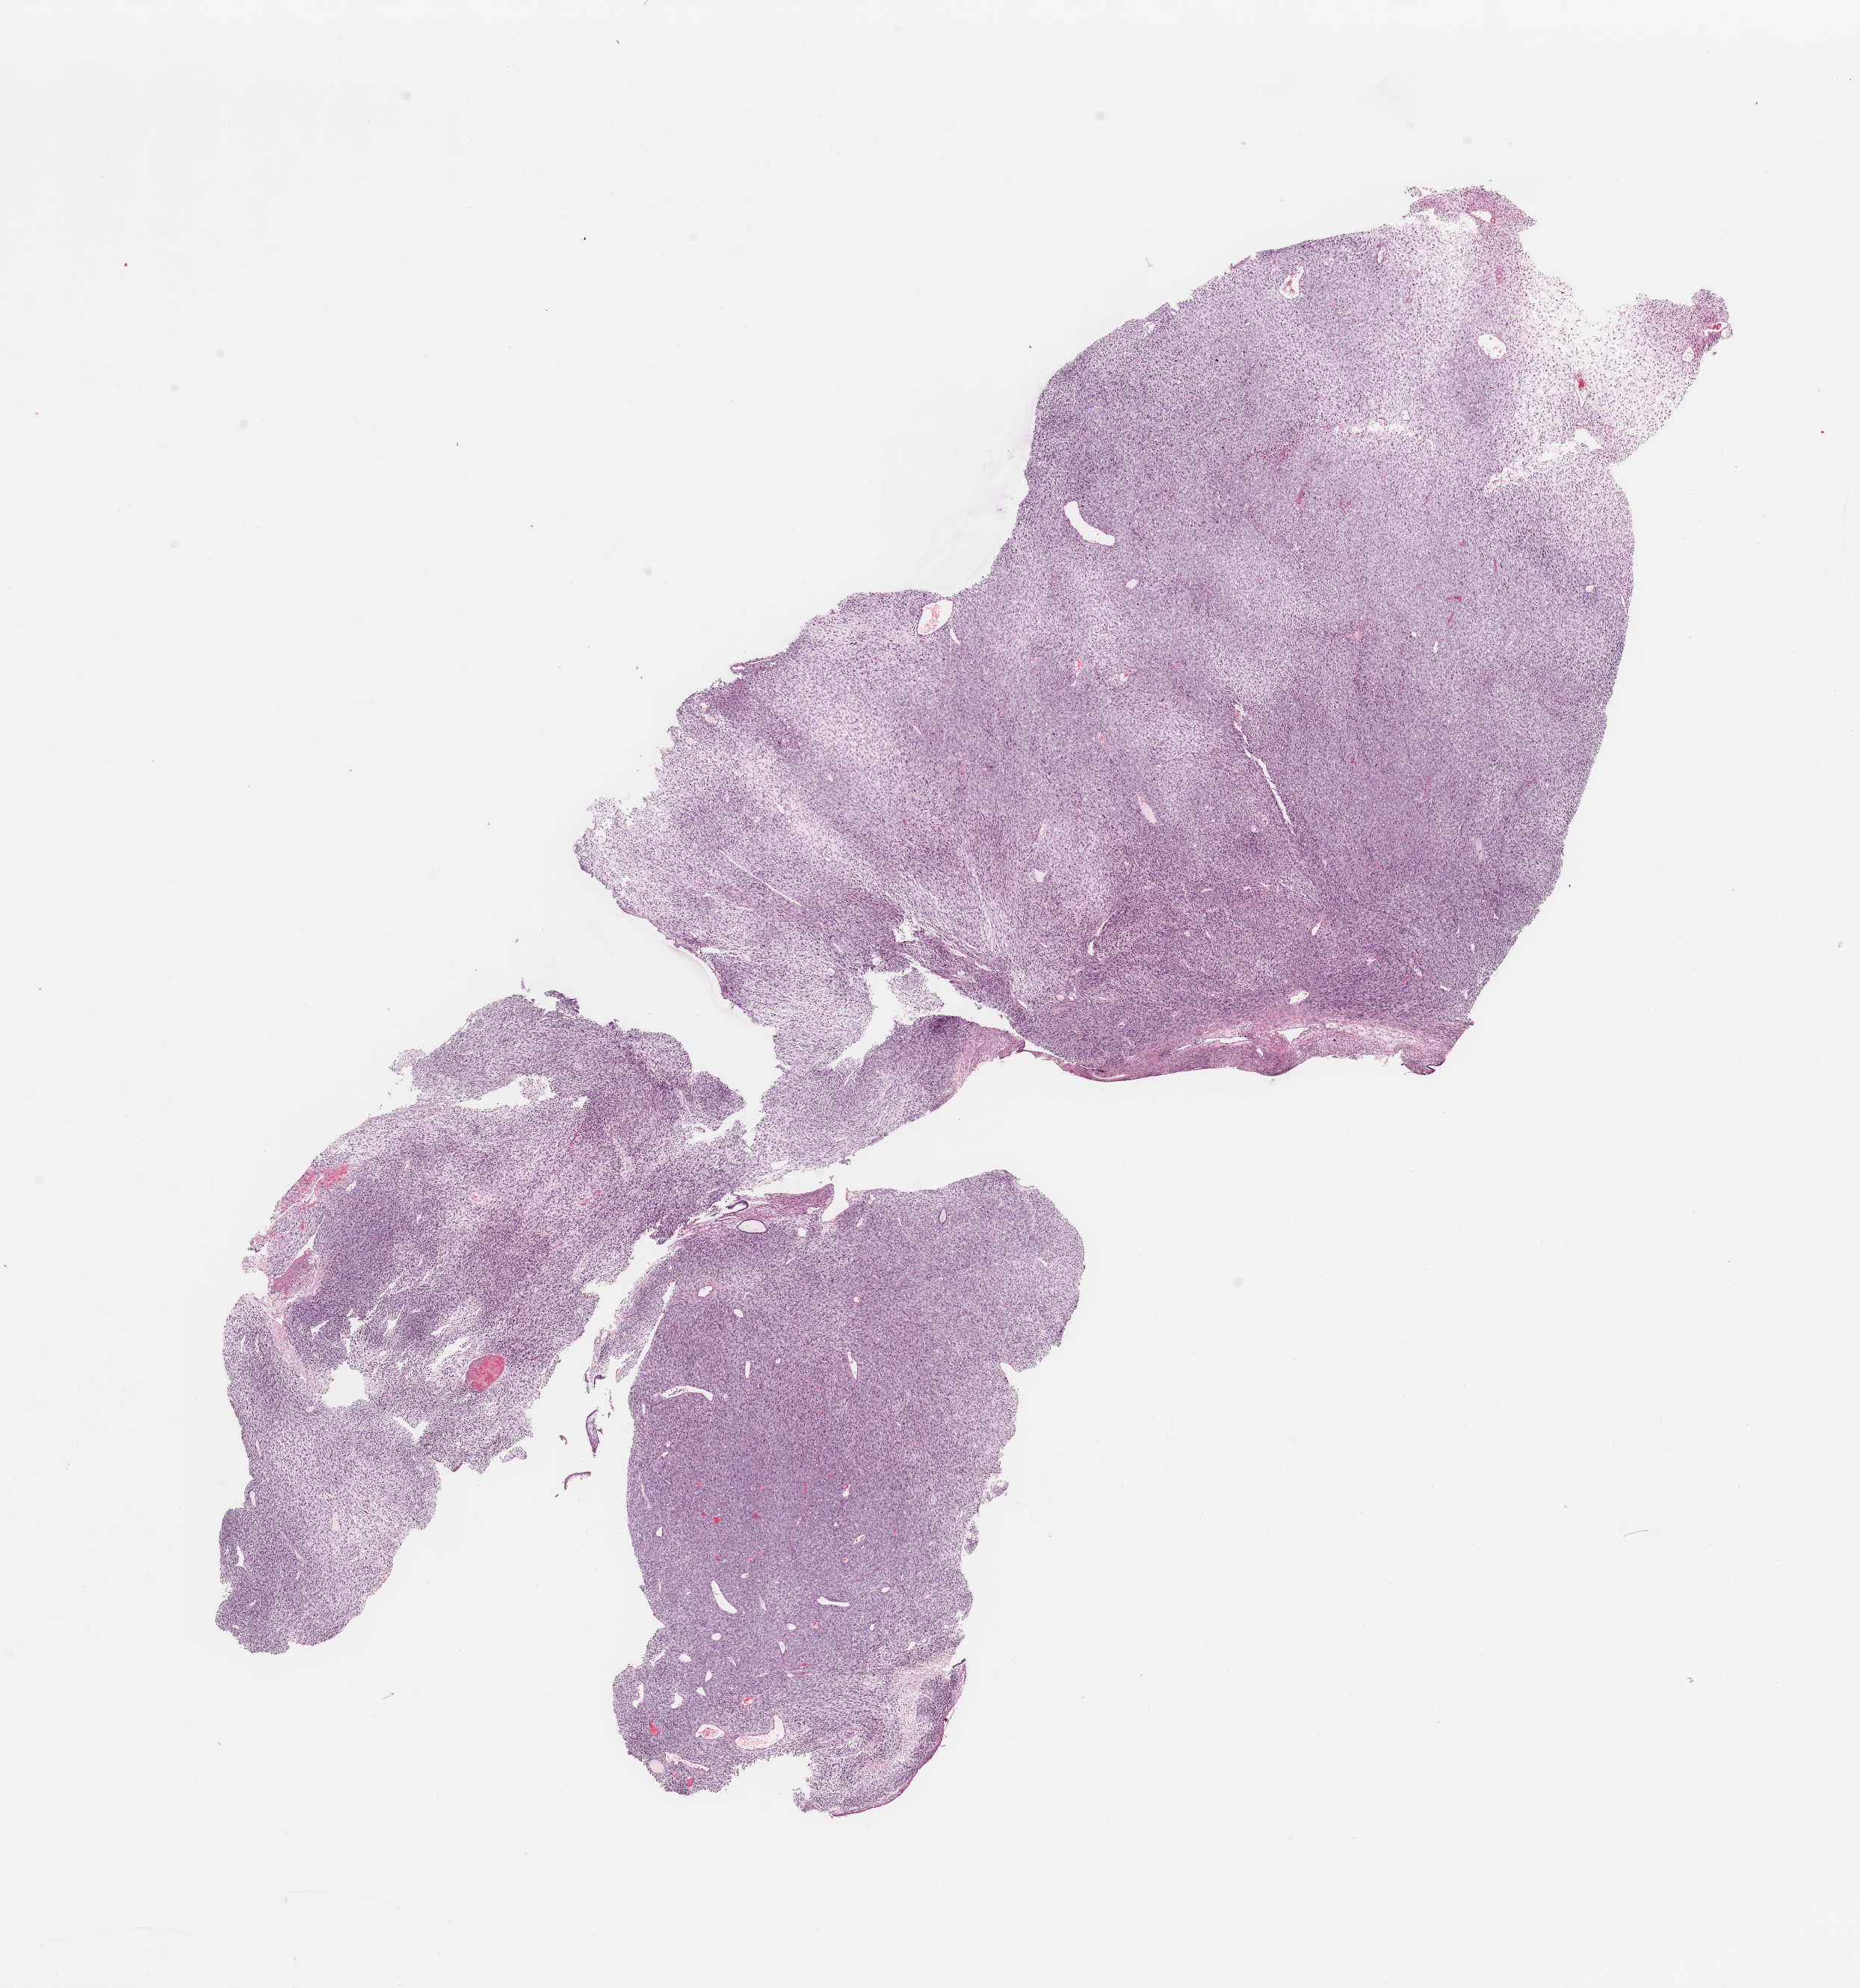
Whole-slide histology image, H&E — low-resolution overview of the scanned area, about 19.7 x 21.0 mm (slide scanned at 20x). Female, 62 y/o.
Patient diagnosis (cohort enrolment): sarcoma (site not recorded at cohort level). Primary tumour site (as recorded): gynecologic.